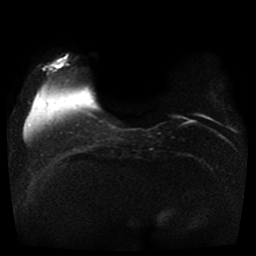
Breast MRI, one axial slice. Slice 7 of 41 in the series (ordered by position). Diffusion-weighted series; image 2 of 4 stored at this slice position (different b-values; order by instance number). 1.5 T. 256 × 256 image matrix. Female patient.
Annotated regions visible in this slice (manually delineated by an expert):
- tumour on diffusion-weighted imaging: bounding box [x1, y1, x2, y2] px = [53, 62, 65, 67]